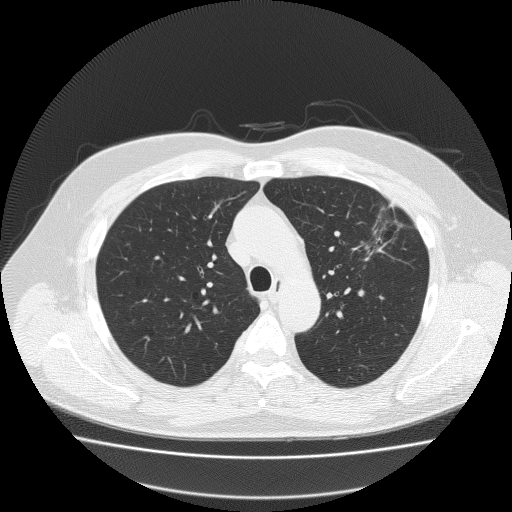
Axial slice from a low-dose chest CT screening exam; baseline annual screen; lung window (W 1500 / L -600 HU); 2 mm slice thickness; lung (sharp) reconstruction kernel (FC51). Male participant, aged 62 years at enrolment. Former smoker at enrolment.
Lesion marked by an expert reader, bounding box [x1, y1, x2, y2] px = [358, 197, 426, 259]. Screening reader's record for this exam (one nodule recorded; not confirmed to be the boxed lesion): non-calcified nodule or mass ≥4 mm, left upper lobe, 18 × 8 mm, spiculated (stellate) margins, soft tissue attenuation. Lung cancer was diagnosed 49 days after this screen: bronchiolo-alveolar adenocarcinoma, NOS, left upper lobe, well differentiated (G1), stage IA (AJCC 6th edition), 25 mm at pathology.